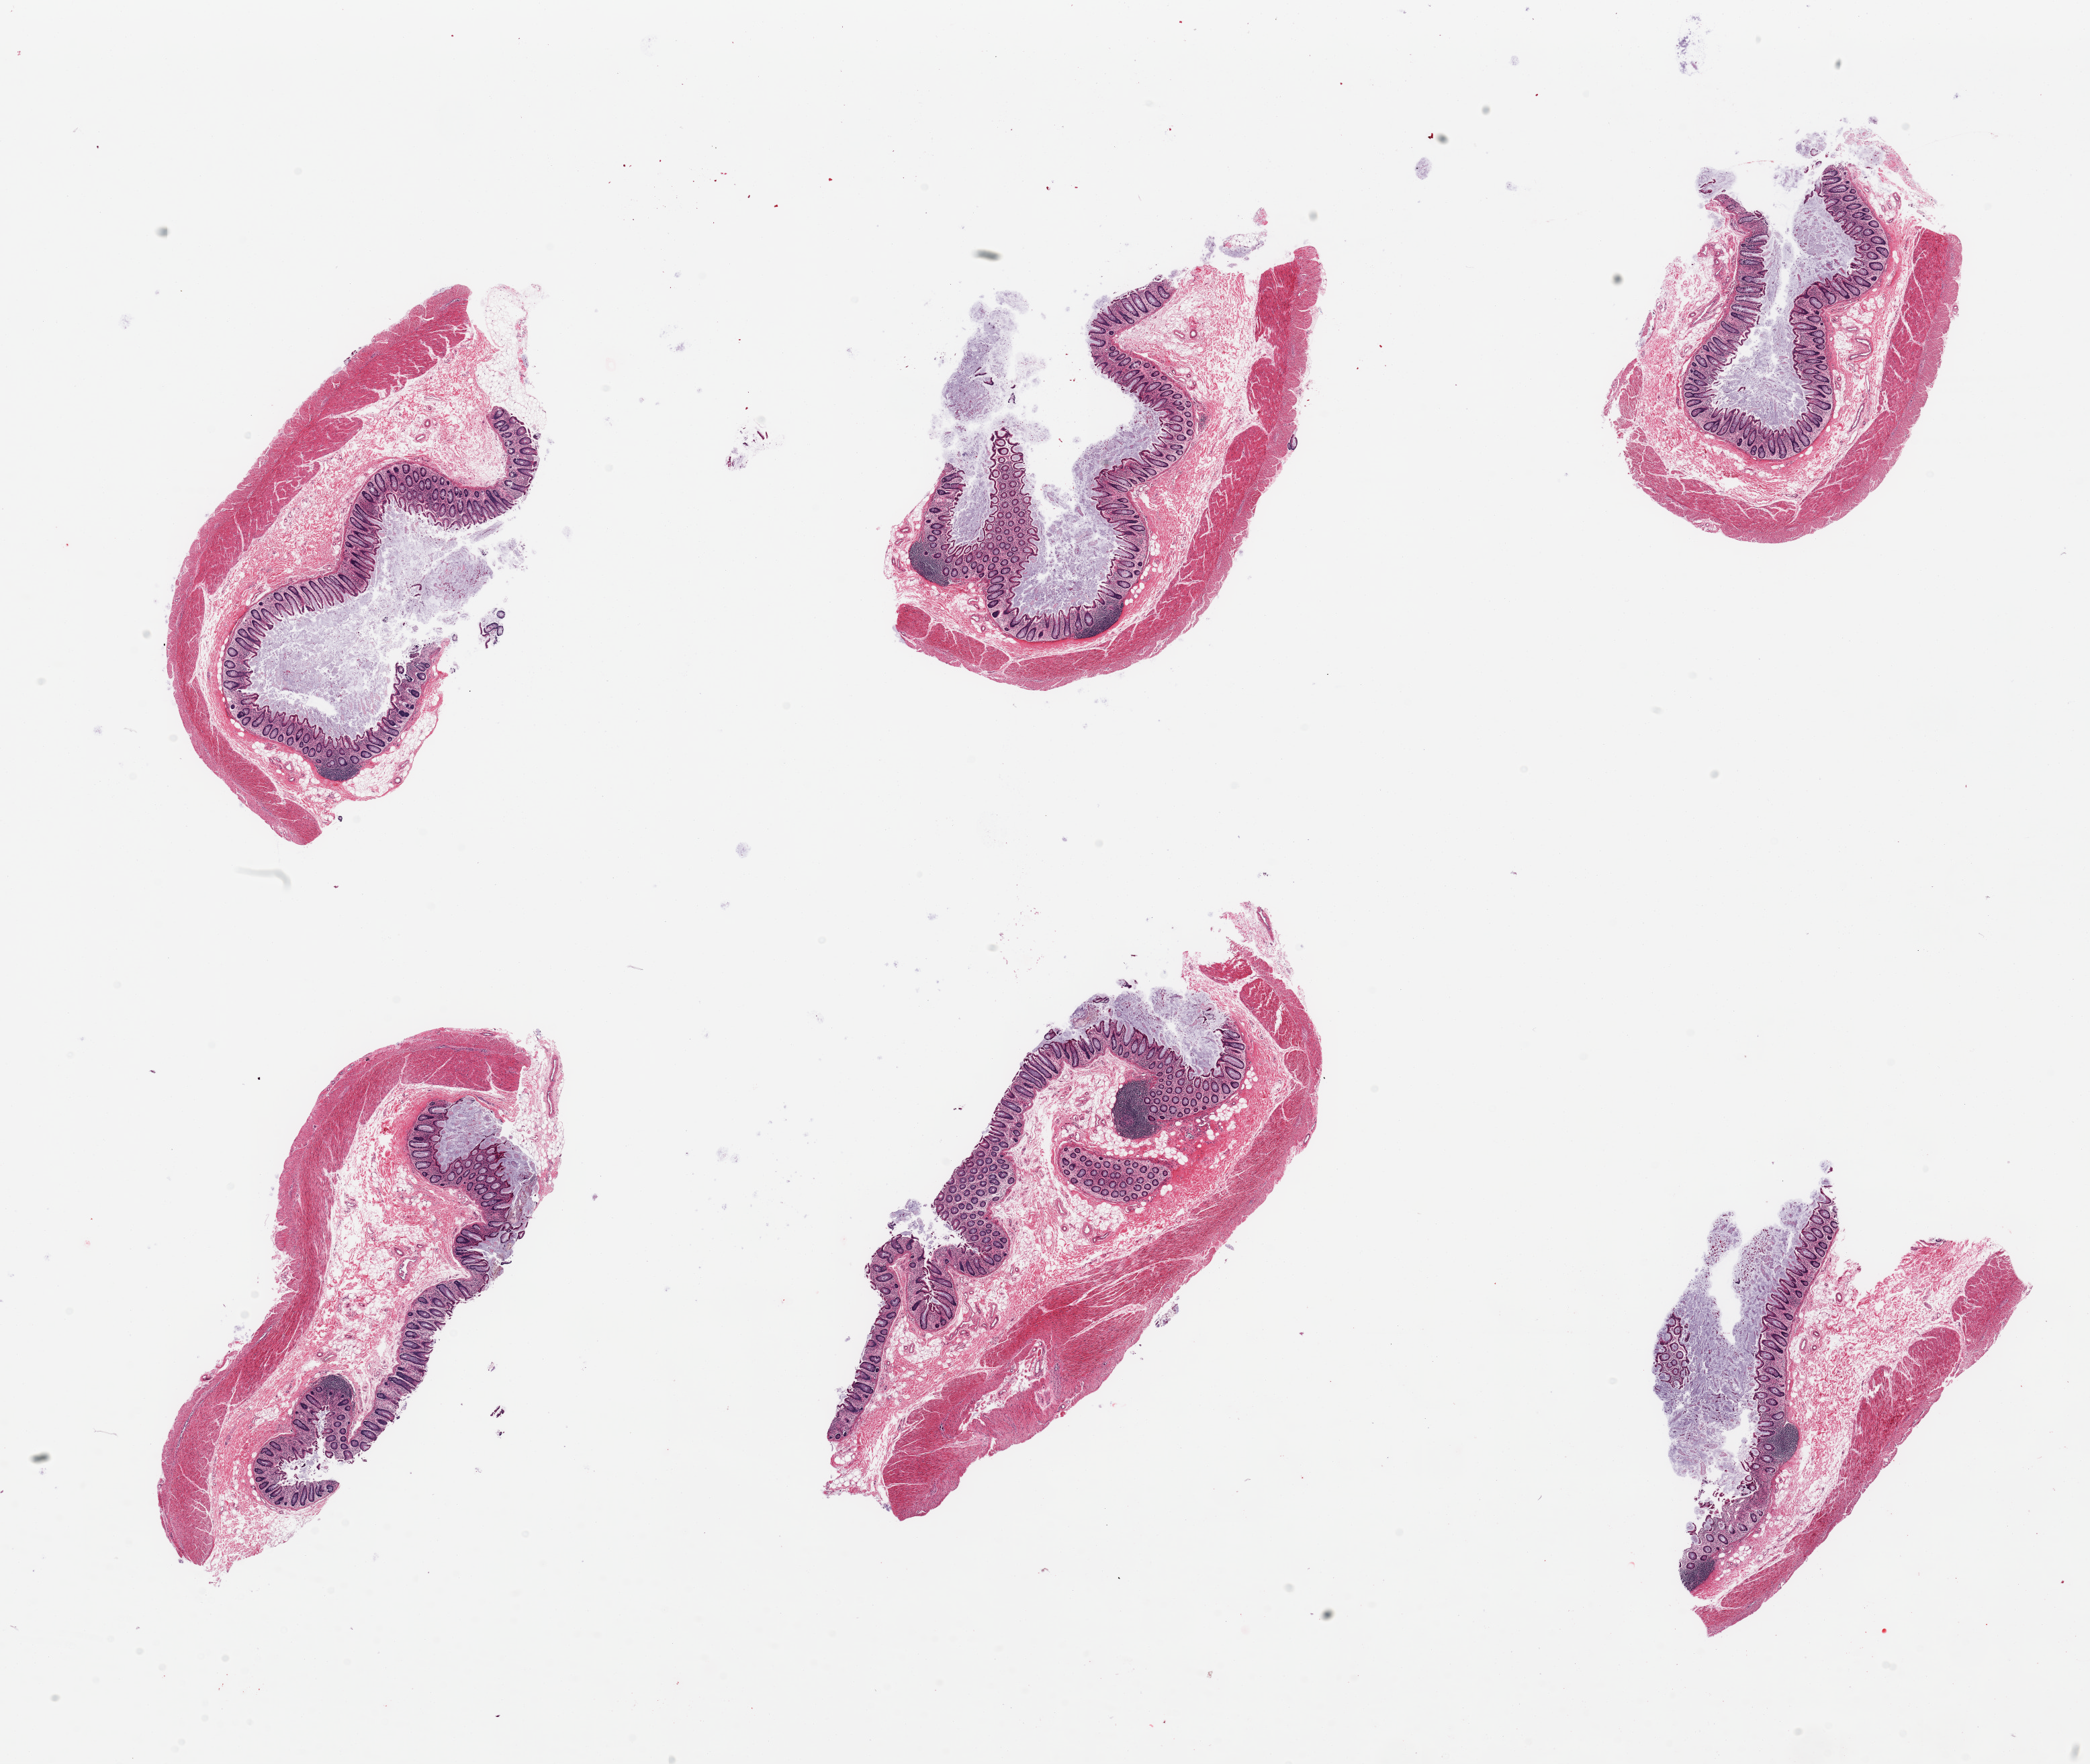
Whole-slide image, hematoxylin and eosin (H&E) stain — shown as a low-resolution overview of the whole scanned area (about 24.6 x 20.8 mm), PAXgene-fixed paraffin-embedded (PFPE) section, section of transverse colon (target tissue), donor tissue sample. Donor sex: male.
Pathologist's review note for this sample: 6 pieces; well preserved; abundant mucus in lumen.